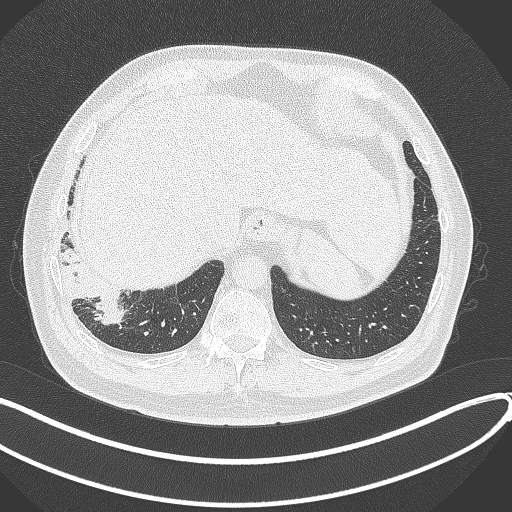
Chest CT, one axial slice. Reconstruction kernel B70f. Lung window (W 1500 / L -600 HU). 512 × 512 image matrix, field of view 400 × 400 mm. Male patient, age 59 years.
Annotated regions visible in this slice (bounding box drawn by a radiologist):
- lung tumour (recorded histology: adenocarcinoma): bounding box [x1, y1, x2, y2] px = [61, 255, 132, 331]